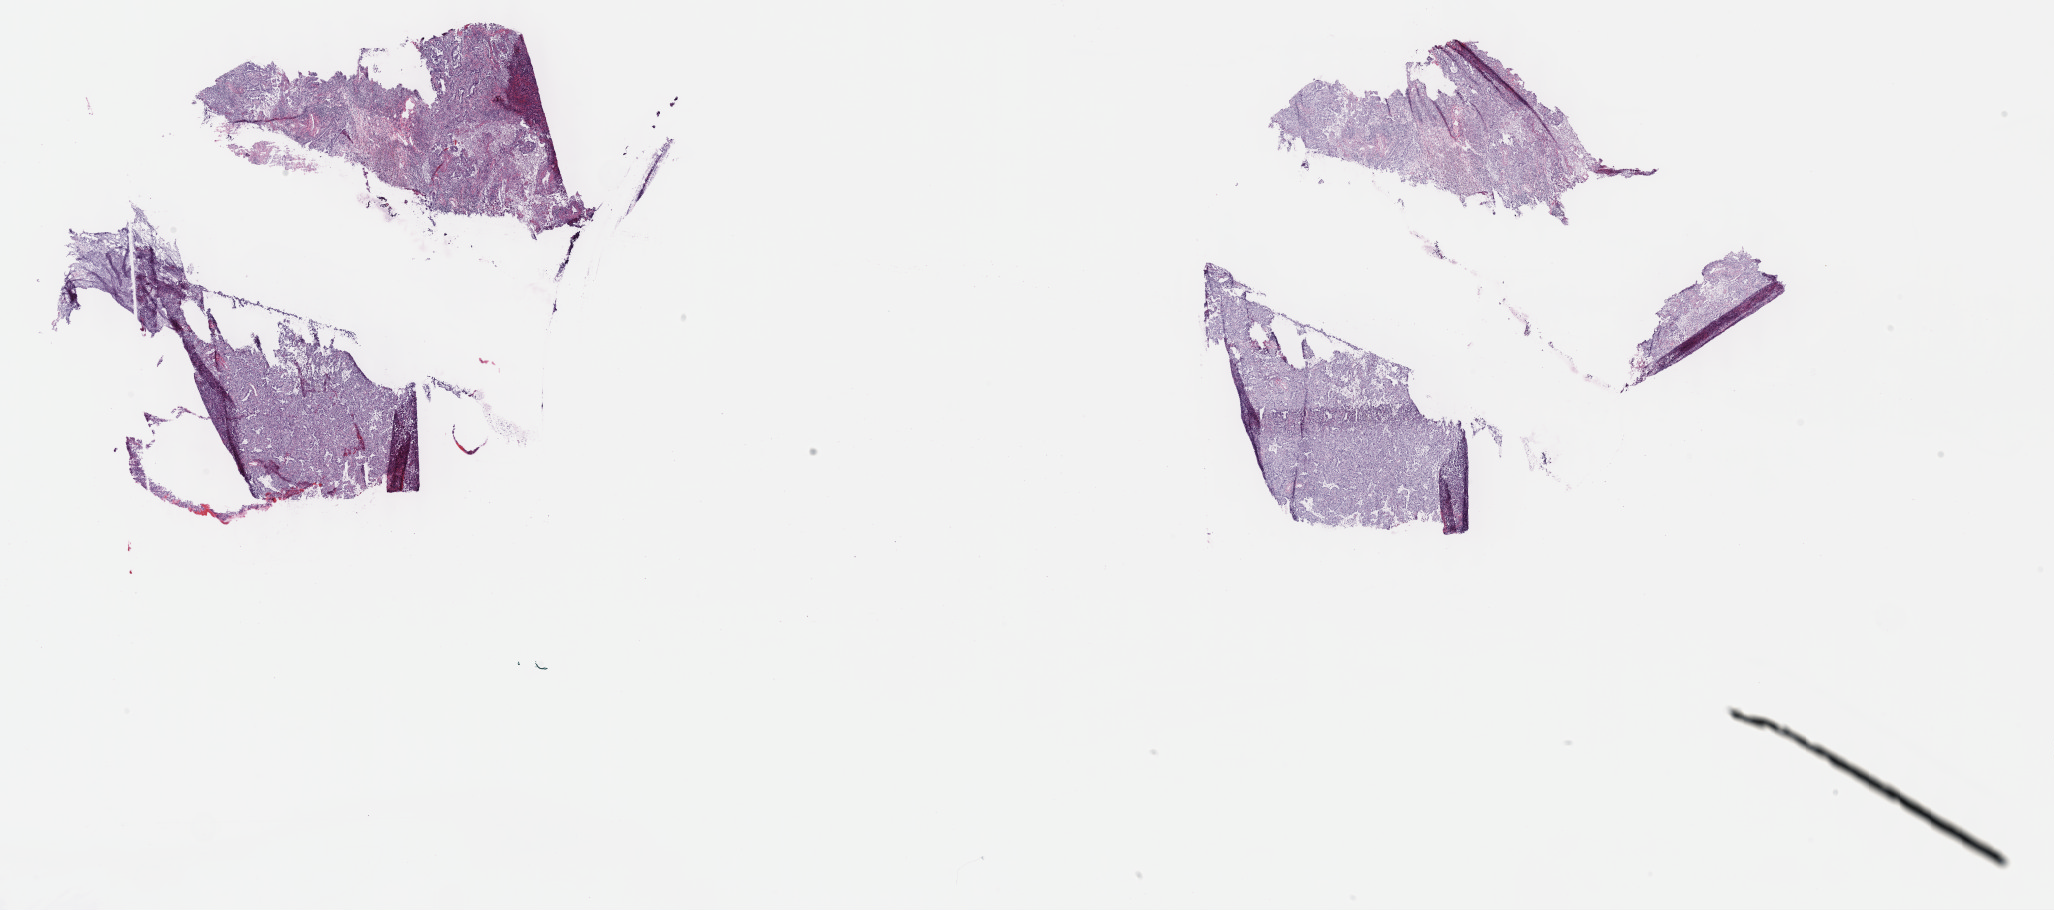
Digitized H&E-stained tissue section (whole slide) — a low-resolution overview of the entire scanned area, about 33.2 x 14.7 mm; frozen section; primary tumour sample from the lung. Male patient; age at initial diagnosis 56 years.
Histologic diagnosis: Adenocarcinoma, NOS (upper lobe, lung).